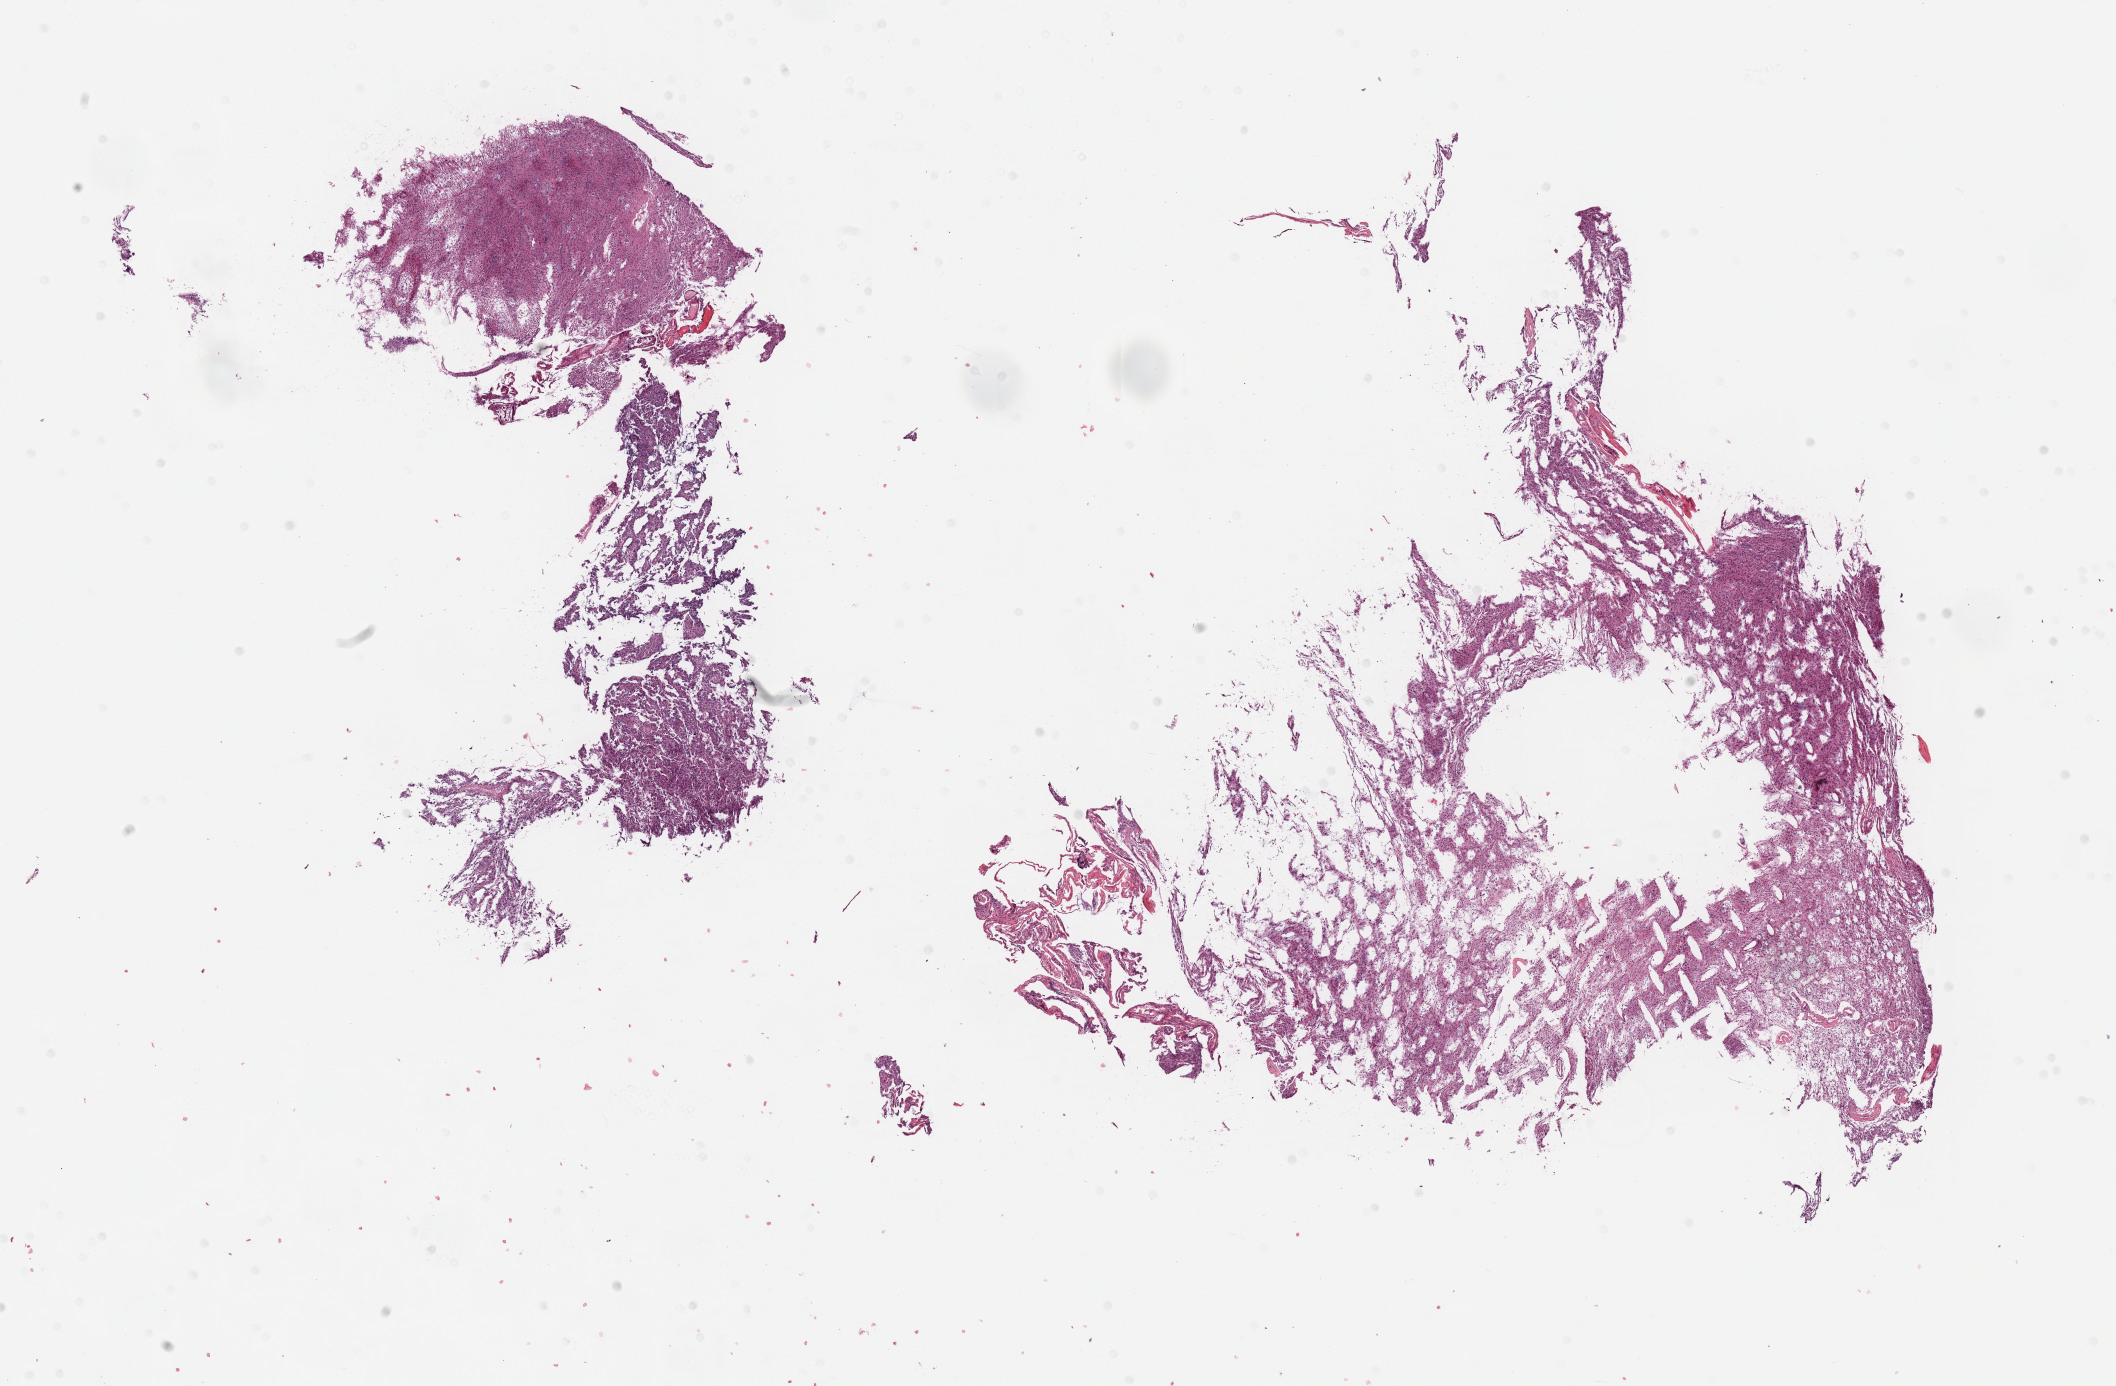
Whole-slide histology image, H&E, whole scanned area (about 17.1 x 11.2 mm) shown as a low-resolution overview. Formalin-fixed paraffin-embedded (FFPE) diagnostic section. Sample: primary tumour, brain. Male, age 28 years at initial diagnosis. Histologic grade: G2 (moderately differentiated).
Laterality: right. Diagnosis: Mixed glioma.